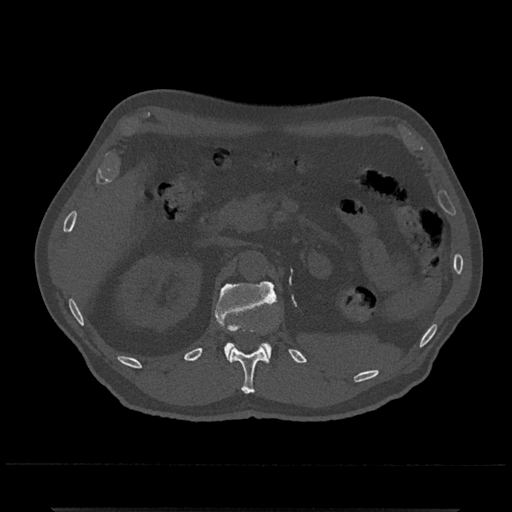
CT including the spine, one axial slice. Position 400 of 797 along the scan axis. 120 kVp. Bone window (W 1800 / L 400 HU). 0.5 mm slice thickness. 512 × 512 image matrix, field of view 393 × 393 mm. Male patient, age 67 years. From the clinical record (not read from this slice): primary cancer: prostate.
Annotated regions visible in this slice (semi-automatically segmented with operator editing):
- L1 vertebra: box from (x=215, y=281) to (x=277, y=362) px
- T12 vertebra: (x=230, y=330)–(x=269, y=394)